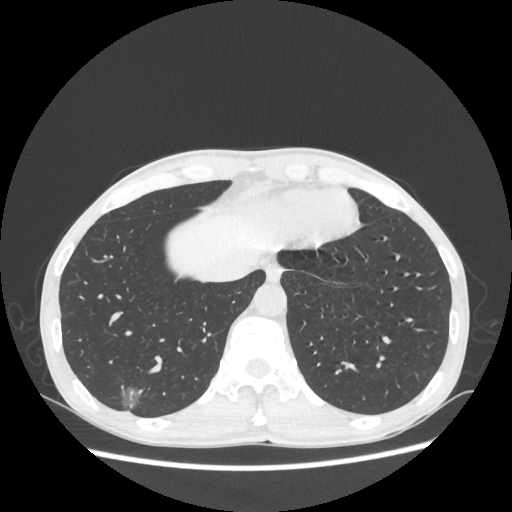
Chest CT, one axial slice; 100 kVp; lung window (W 1500 / L -600 HU); 1.25 mm slice thickness; 512 × 512 image matrix, field of view 360 × 360 mm. Male patient, age 60 years. Case-level facts recorded for this patient, not image findings: clinical TNM (as recorded): T1c N0 M0.
Outlined on this slice (bounding box drawn by a radiologist):
- lung tumour (recorded histology: adenocarcinoma): bounding box (x1, y1, x2, y2) in pixels: (113, 379, 151, 414)